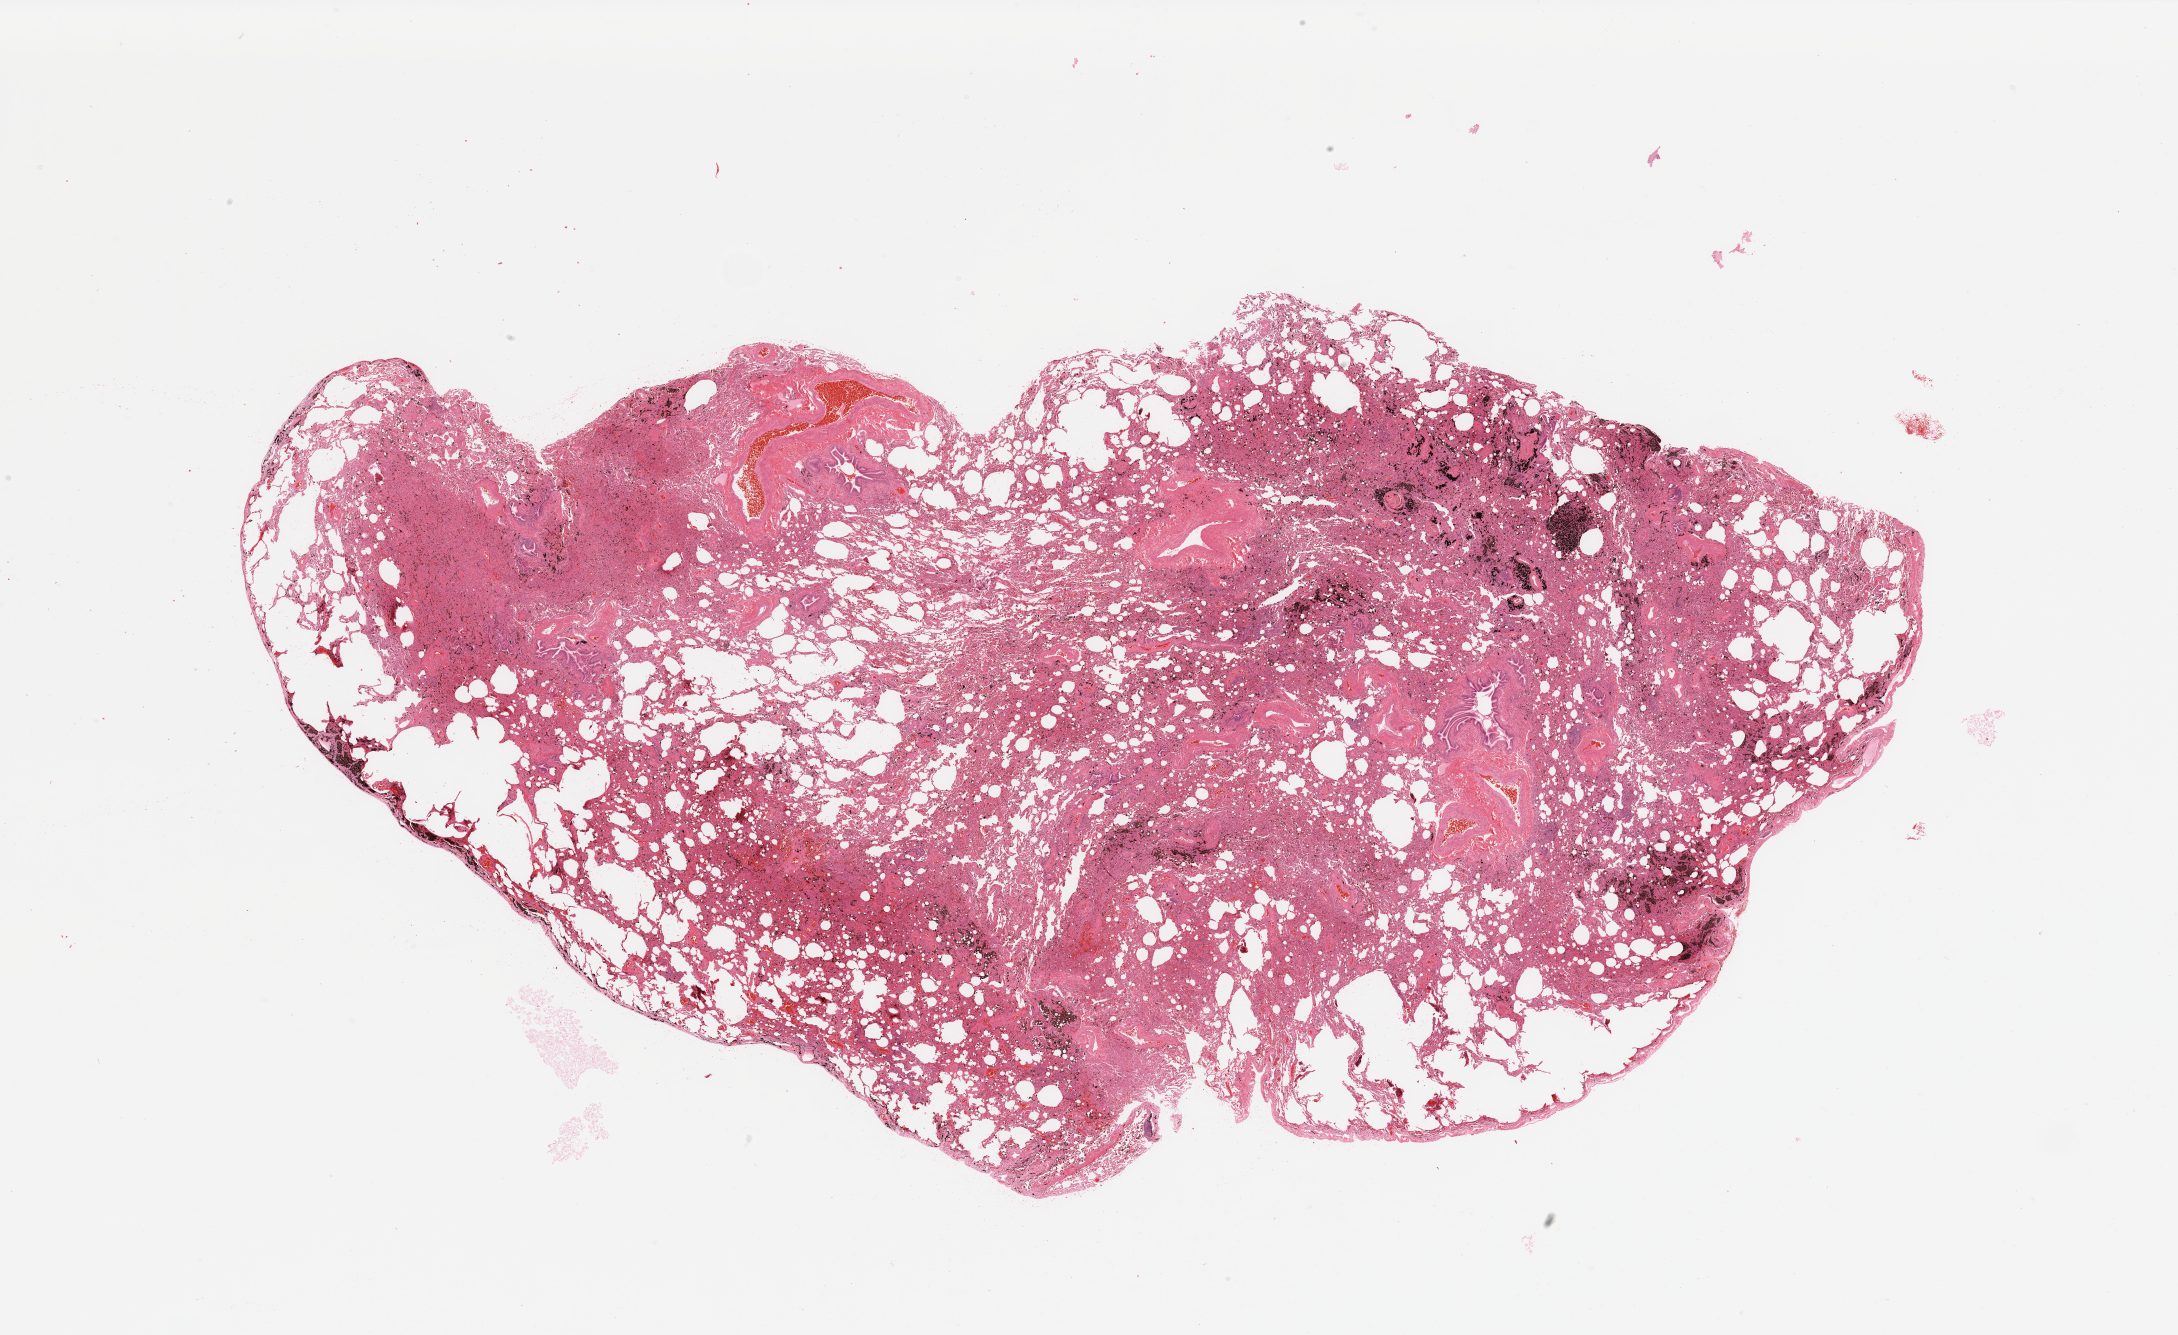
Whole-slide histology image, Hematoxylin and eosin (H&E) stained — shown as a low-resolution overview of the whole scanned area (about 34.5 x 21.1 mm). Normal (non-tumour) tissue sample, sampled site: lung. Patient: male, age 57 years.
• this section: normal (non-tumour) tissue from the same patient
• patient diagnosis: Adenocarcinoma, NOS